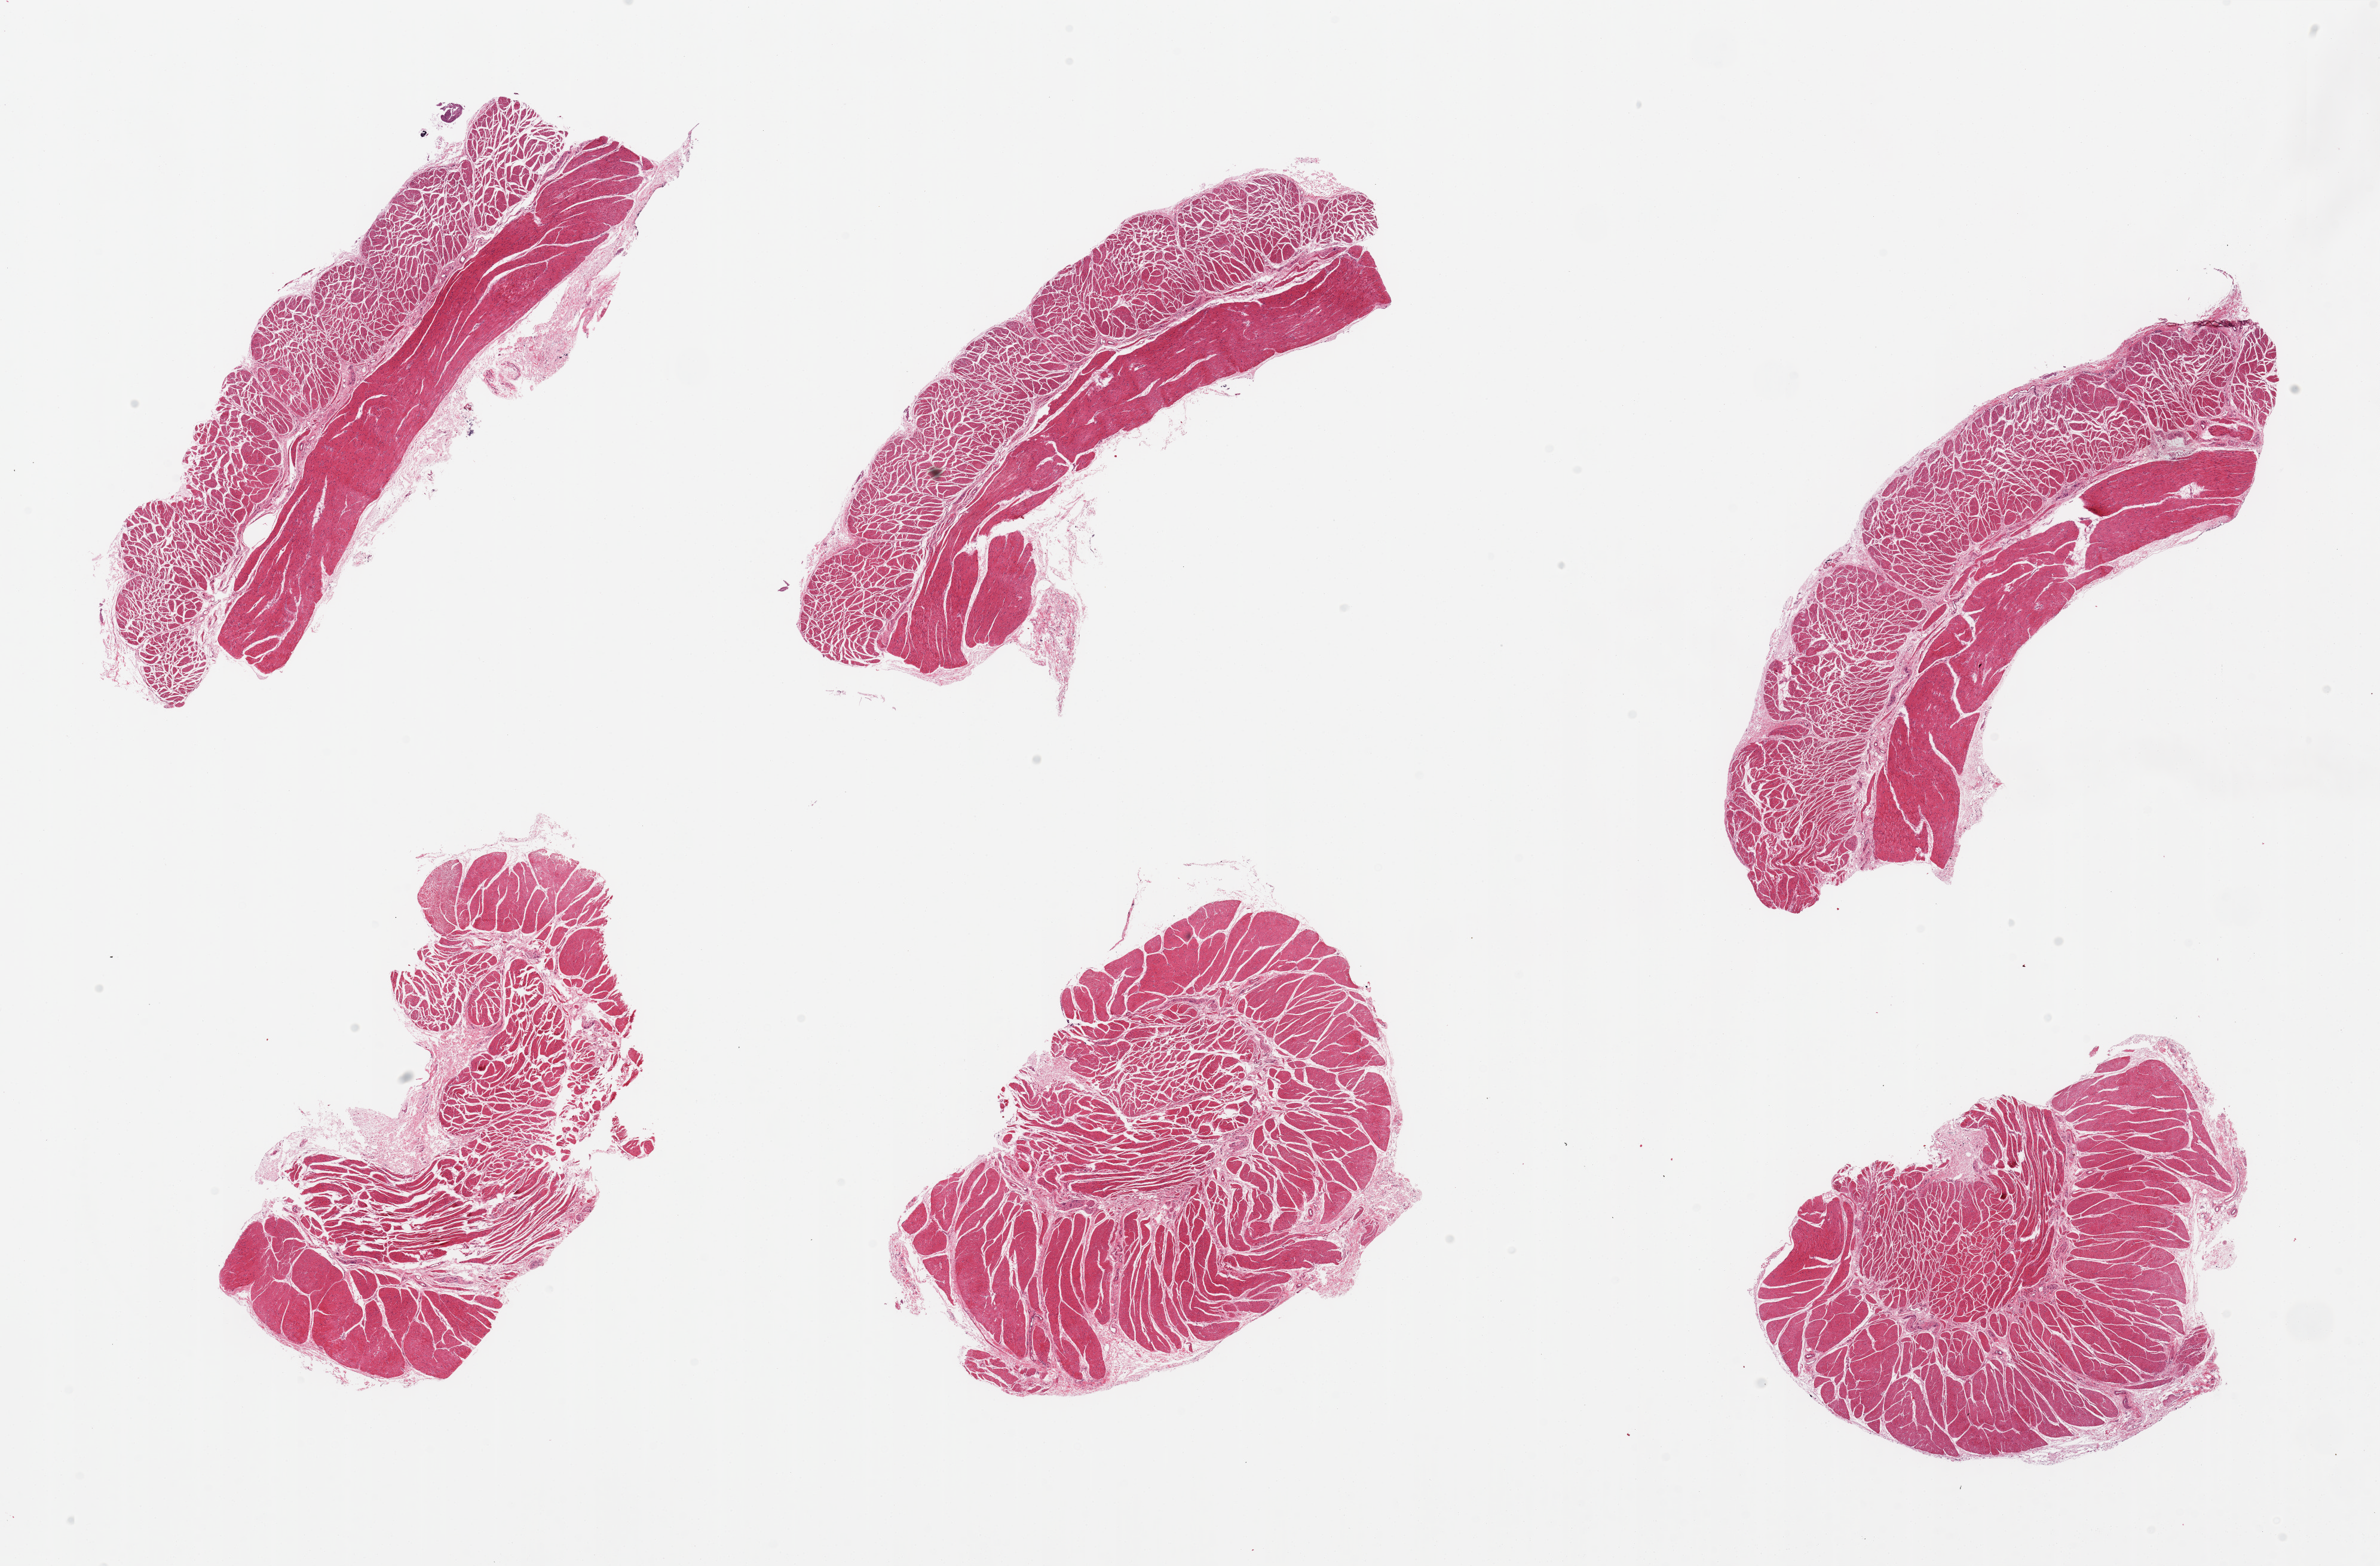
Whole-slide image, H&E stain, whole scanned area (about 31.5 x 20.7 mm, slide scanned at 20x) shown as a low-resolution overview. PAXgene-fixed, paraffin-embedded tissue. Target tissue: esophageal muscle. Donor tissue sample. Male donor.
Reviewer comment on this tissue sample: 6 pieces; well trimmed.